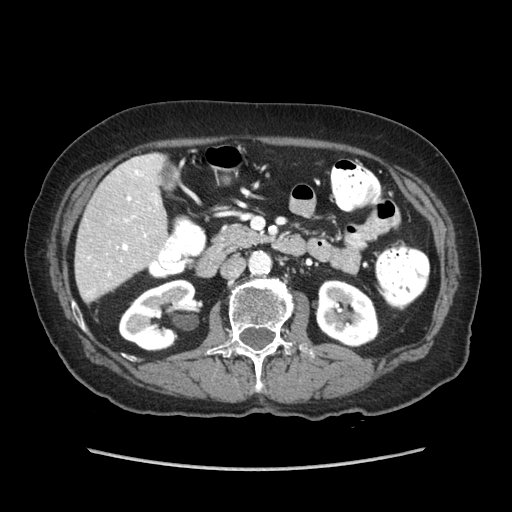
Contrast-enhanced abdominal CT (liver protocol), one axial slice. Slice 24 of 89 in the series (ordered by position). Reconstruction kernel STANDARD. Soft-tissue window (W 400 / L 40 HU). 2.5 mm slice thickness. 512 × 512 image matrix. From the clinical record (not read from this slice): diagnosis: hepatocellular carcinoma (patient treated with transarterial chemoembolisation; whether this scan precedes or follows treatment is not stated here); TNM stage (as recorded): Stage-IIIA; Child-Pugh class: A; tumour nodularity: multinodular.
Outlined on this slice (semi-automatic segmentation, software-assisted and operator-edited):
- liver parenchyma outside the tumour (the mass and vessels are separate outlines, so this box may not span the whole liver): bounding box [x1, y1, x2, y2] px = [74, 153, 166, 302]
- liver vessels: [108, 170, 158, 276]